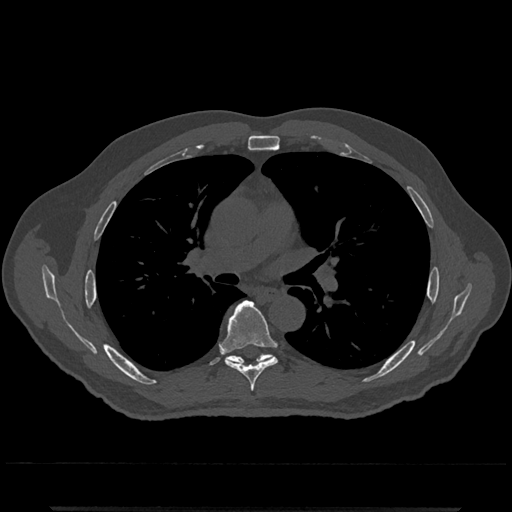
CT including the spine, one axial slice. Position 761 of 797 along the scan axis. Bone window (W 1800 / L 400 HU). 0.5 mm slice thickness. 512 × 512 image matrix, field of view 393 × 393 mm. Patient: male, 67 years. From the clinical record (not read from this slice): primary cancer: prostate.
Outlined on this slice (semi-automatically segmented with operator editing):
- T6 vertebra: bounding box [x1, y1, x2, y2] px = [220, 301, 278, 398]
- T7 vertebra: [227, 354, 272, 365]